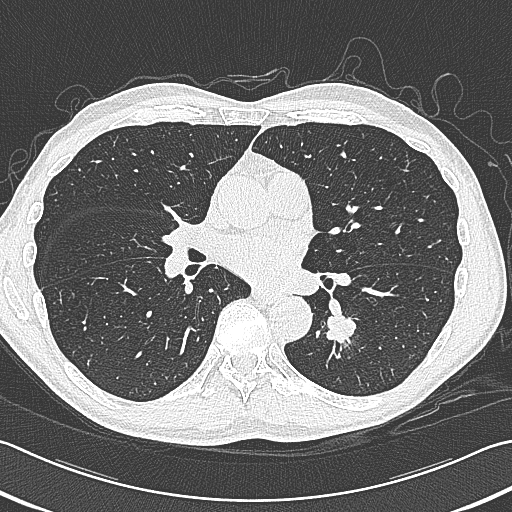
Chest CT (low-dose screening protocol), one axial image. First (baseline) screen. Lung window (W 1500 / L -600 HU). Lung (sharp) reconstruction kernel (B80f). Male participant, aged 59 years at enrolment. Former smoker at enrolment.
Expert-annotated lung lesion, box from (x=313, y=295) to (x=376, y=353) px. Reader record for this screening exam (exam-level; its link to the box is not recorded): non-calcified nodule or mass ≥4 mm, left lower lobe, 15 × 15 mm, smooth margins, soft tissue attenuation. Official screen result: positive, change unspecified: nodule(s) >= 4 mm or enlarging nodule(s), mass(es), or other non-specific abnormalities suspicious for lung cancer. Participant outcome: lung cancer diagnosed 17 days after this screen — squamous cell carcinoma, large cell, nonkeratinizing, NOS, left lower lobe, poorly differentiated (G3), stage IB (AJCC 6th edition), 31 mm at pathology.